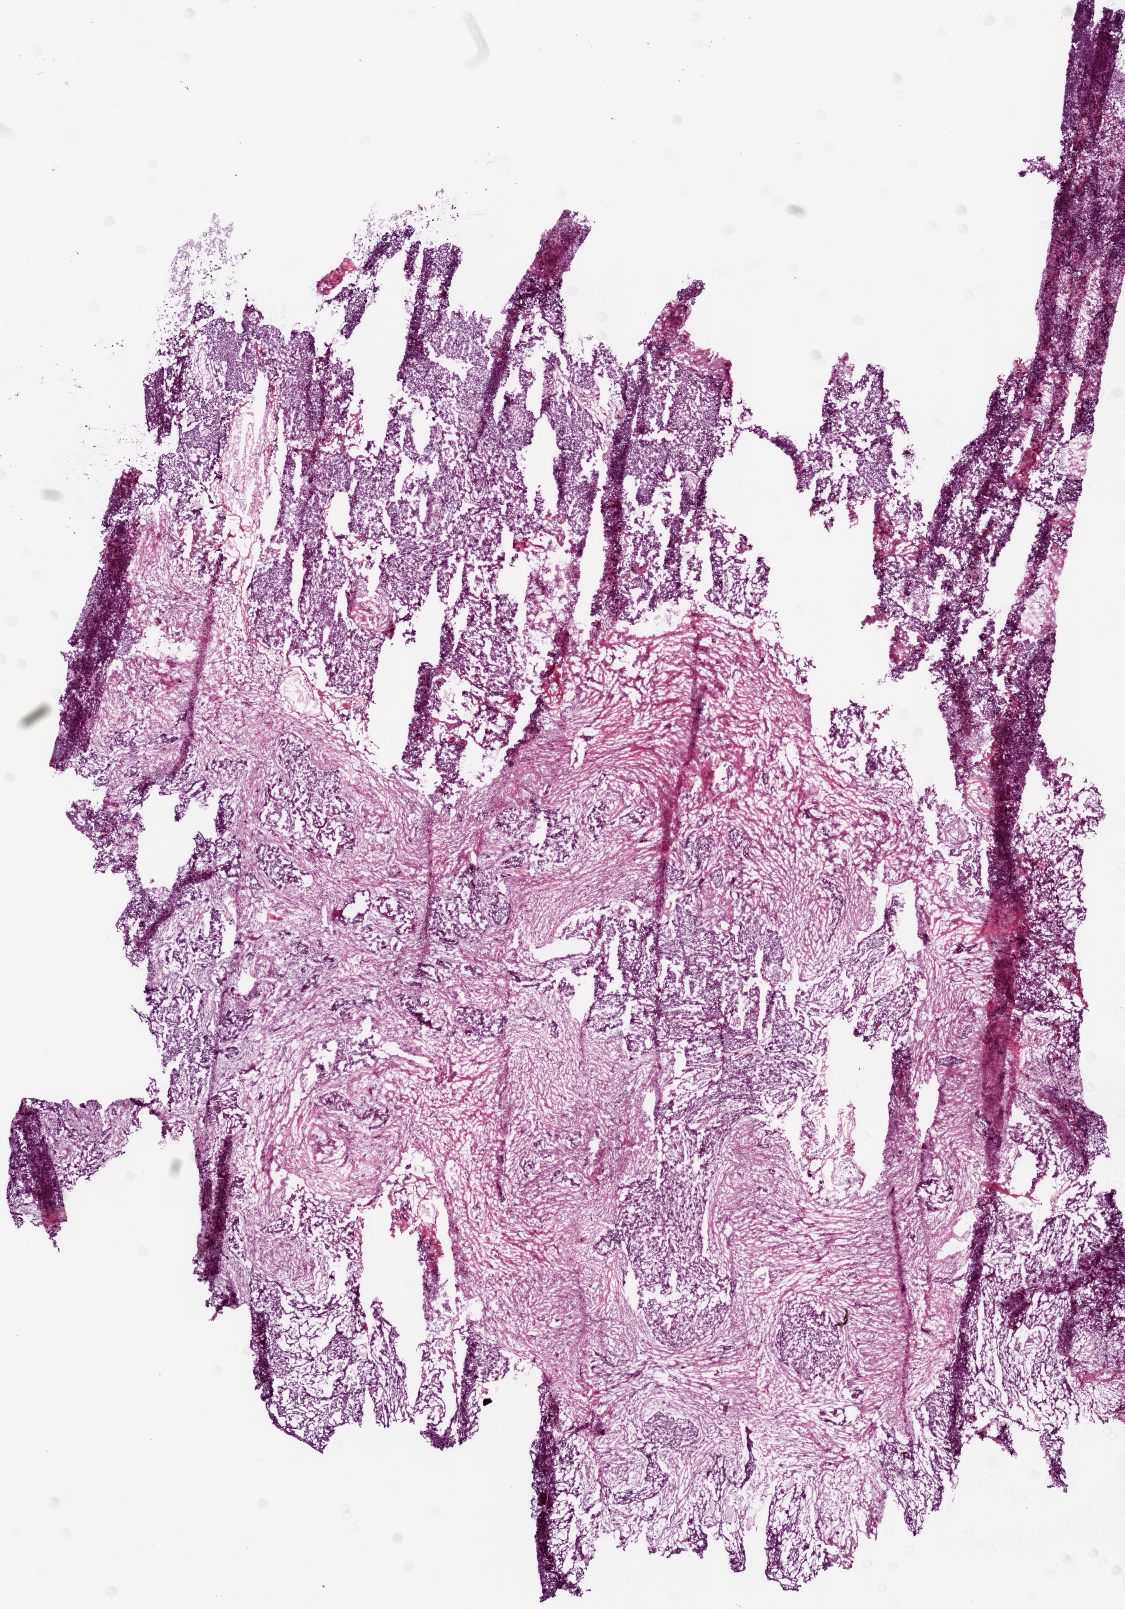
Digitized Hematoxylin and eosin (H&E) stained tissue section (whole slide) — shown as a low-resolution overview of the whole scanned area (about 9.0 x 12.9 mm); frozen section; primary tumour sample from the ovary. Female patient; age at initial diagnosis 66 years. Histologic grade: G3 (poorly differentiated). Pathologist review of this section (percent, as recorded): tumour cells 69%, tumour nuclei 70%, normal cells 0%, stromal cells 30%, necrosis 1%.
• laterality: left
• pathologic diagnosis: Serous cystadenocarcinoma, NOS
• FIGO stage: IIIC